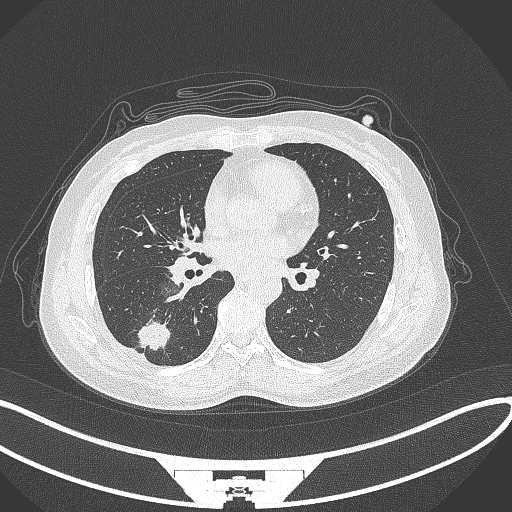
Chest CT, one axial slice. Slice 142 of 352 in the series (ordered by position). 120 kVp. Lung window (W 1500 / L -600 HU). 1 mm slice thickness. 512 × 512 image matrix, field of view 400 × 400 mm. Patient: female, 55 years. Case-level facts recorded for this patient, not image findings: clinical TNM (as recorded): T1c N1 M0.
Annotated regions visible in this slice (bounding box drawn by a radiologist):
- lung tumour (recorded histology: adenocarcinoma): bounding box <130,314,173,352> (left, top, right, bottom; pixels)